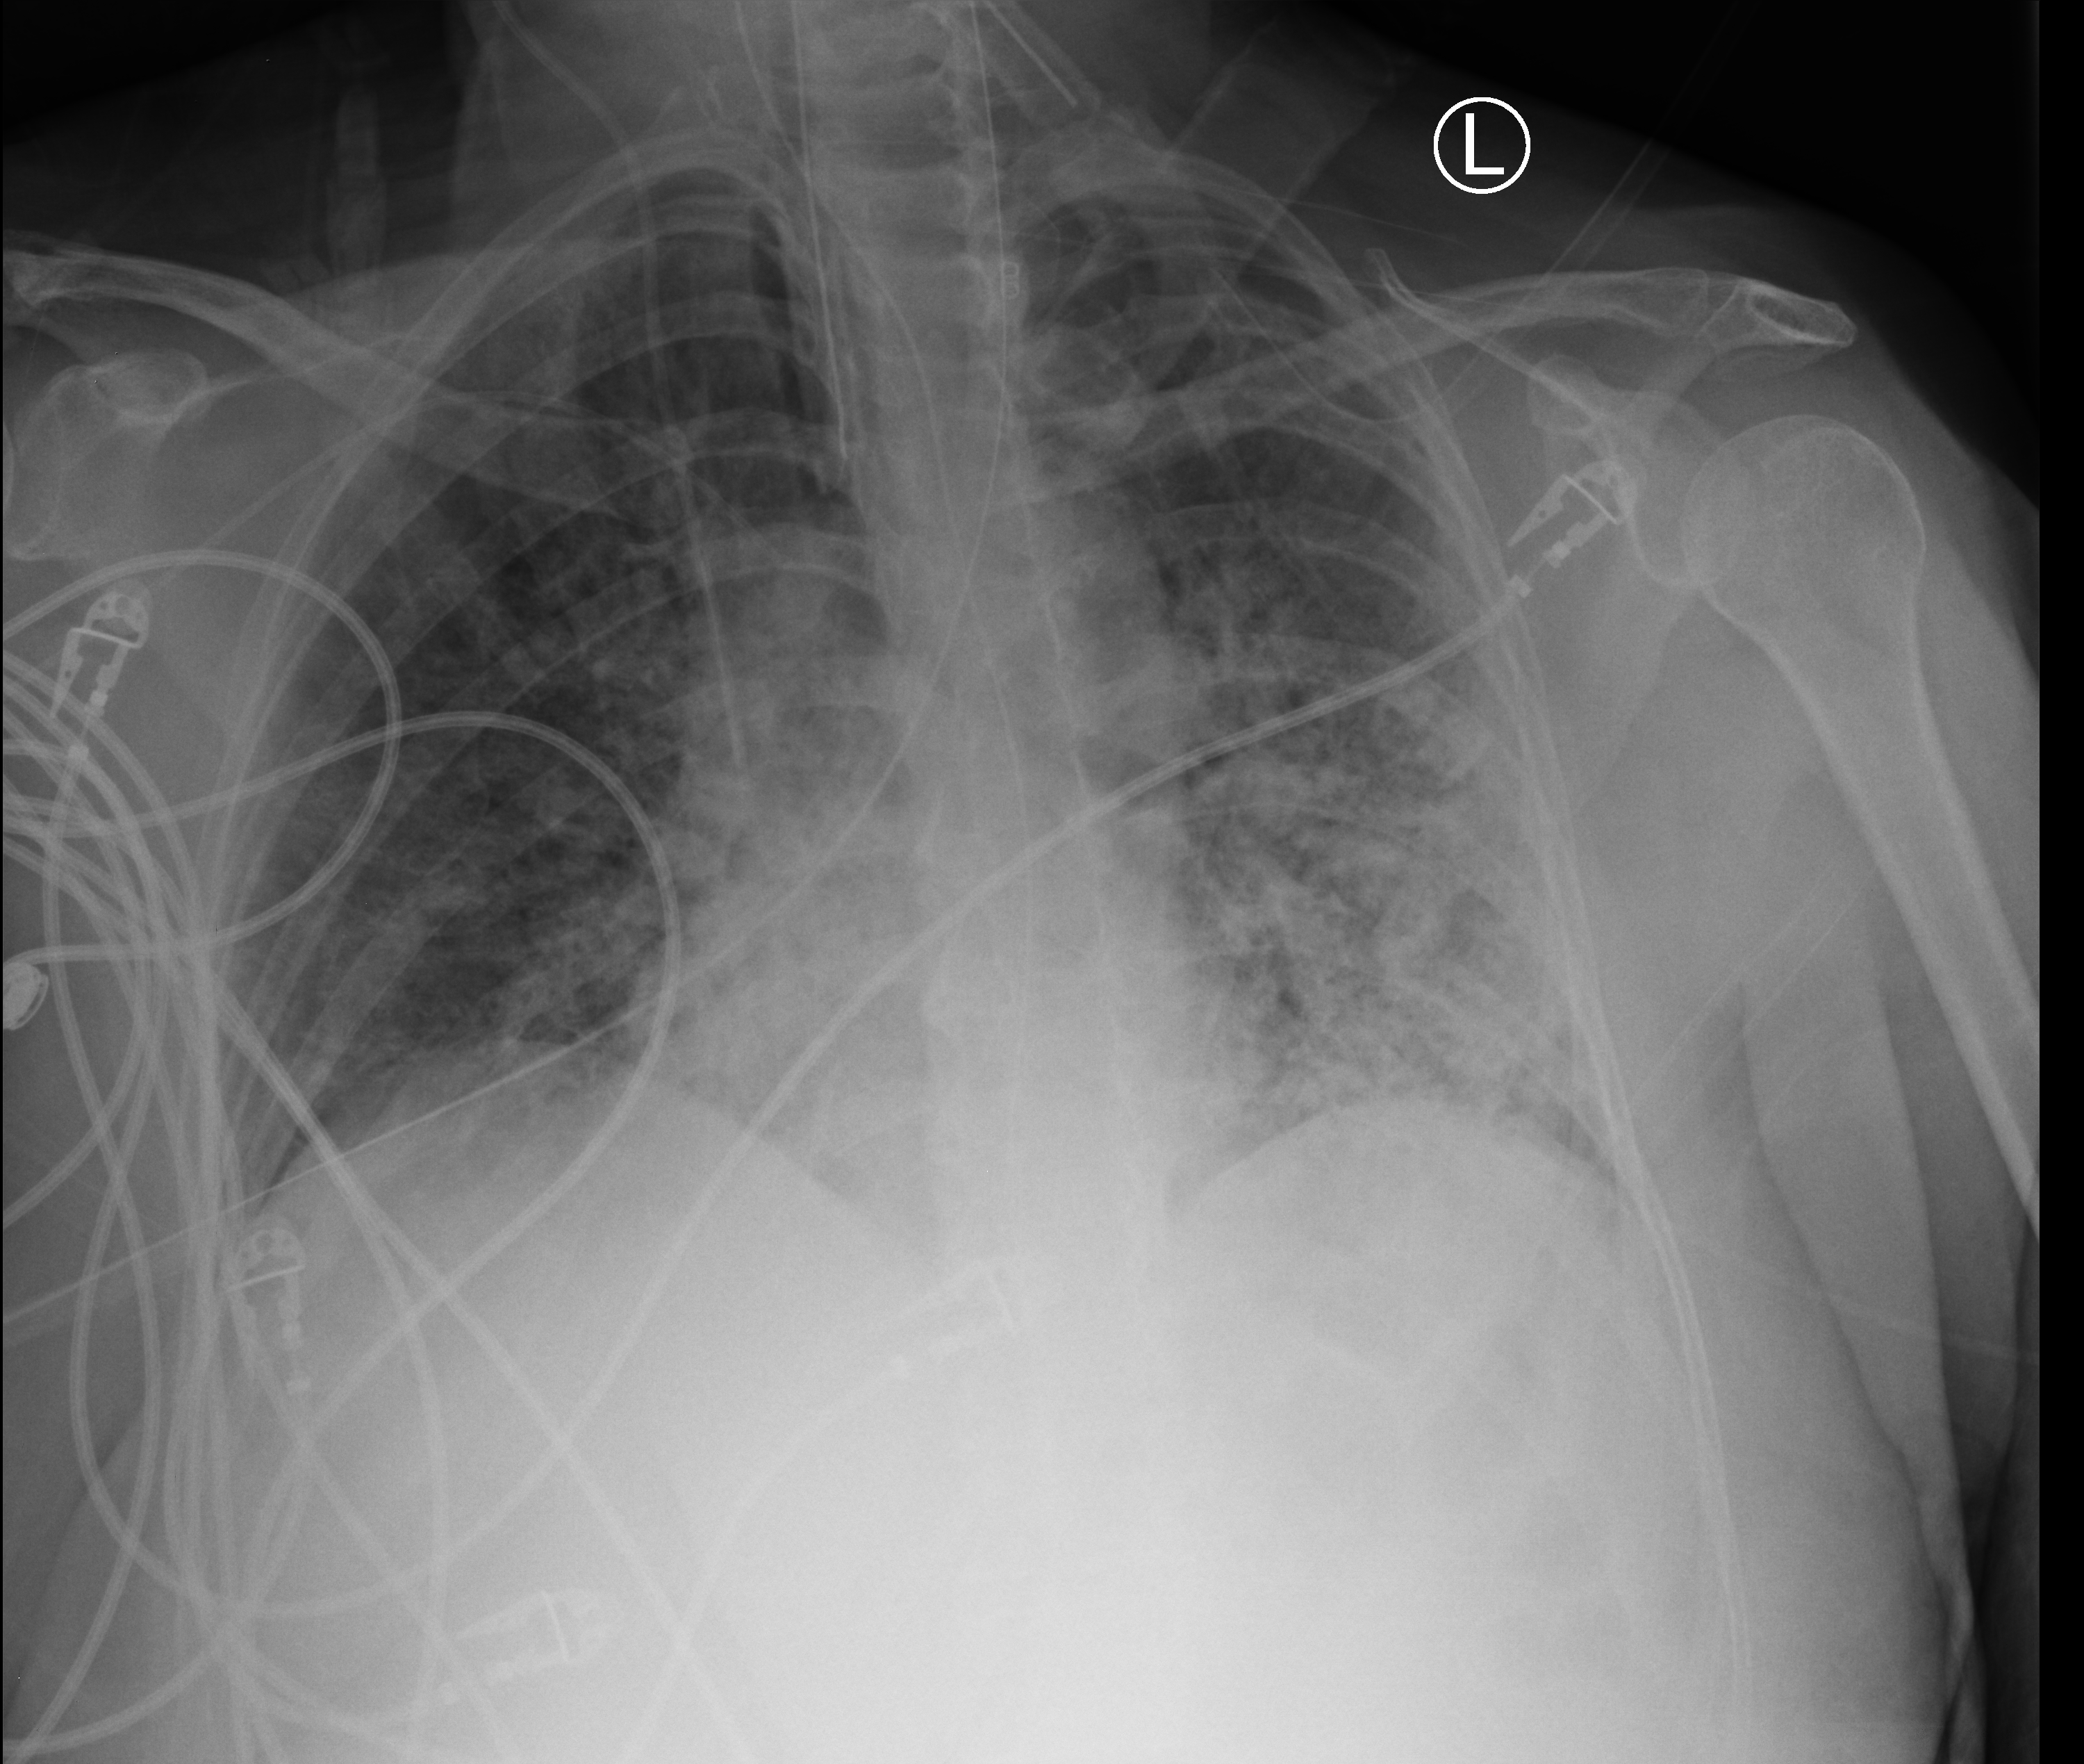
Bedside chest radiograph (computed radiography). Female patient hospitalised with COVID-19, age 60–74 years.
Hospital-stay facts (about this admission, not read from this image; timing relative to this image not recorded):
- length of hospital stay: 43 days
- mechanically ventilated during this hospital stay: yes
- admitted to intensive care during this hospital stay: yes